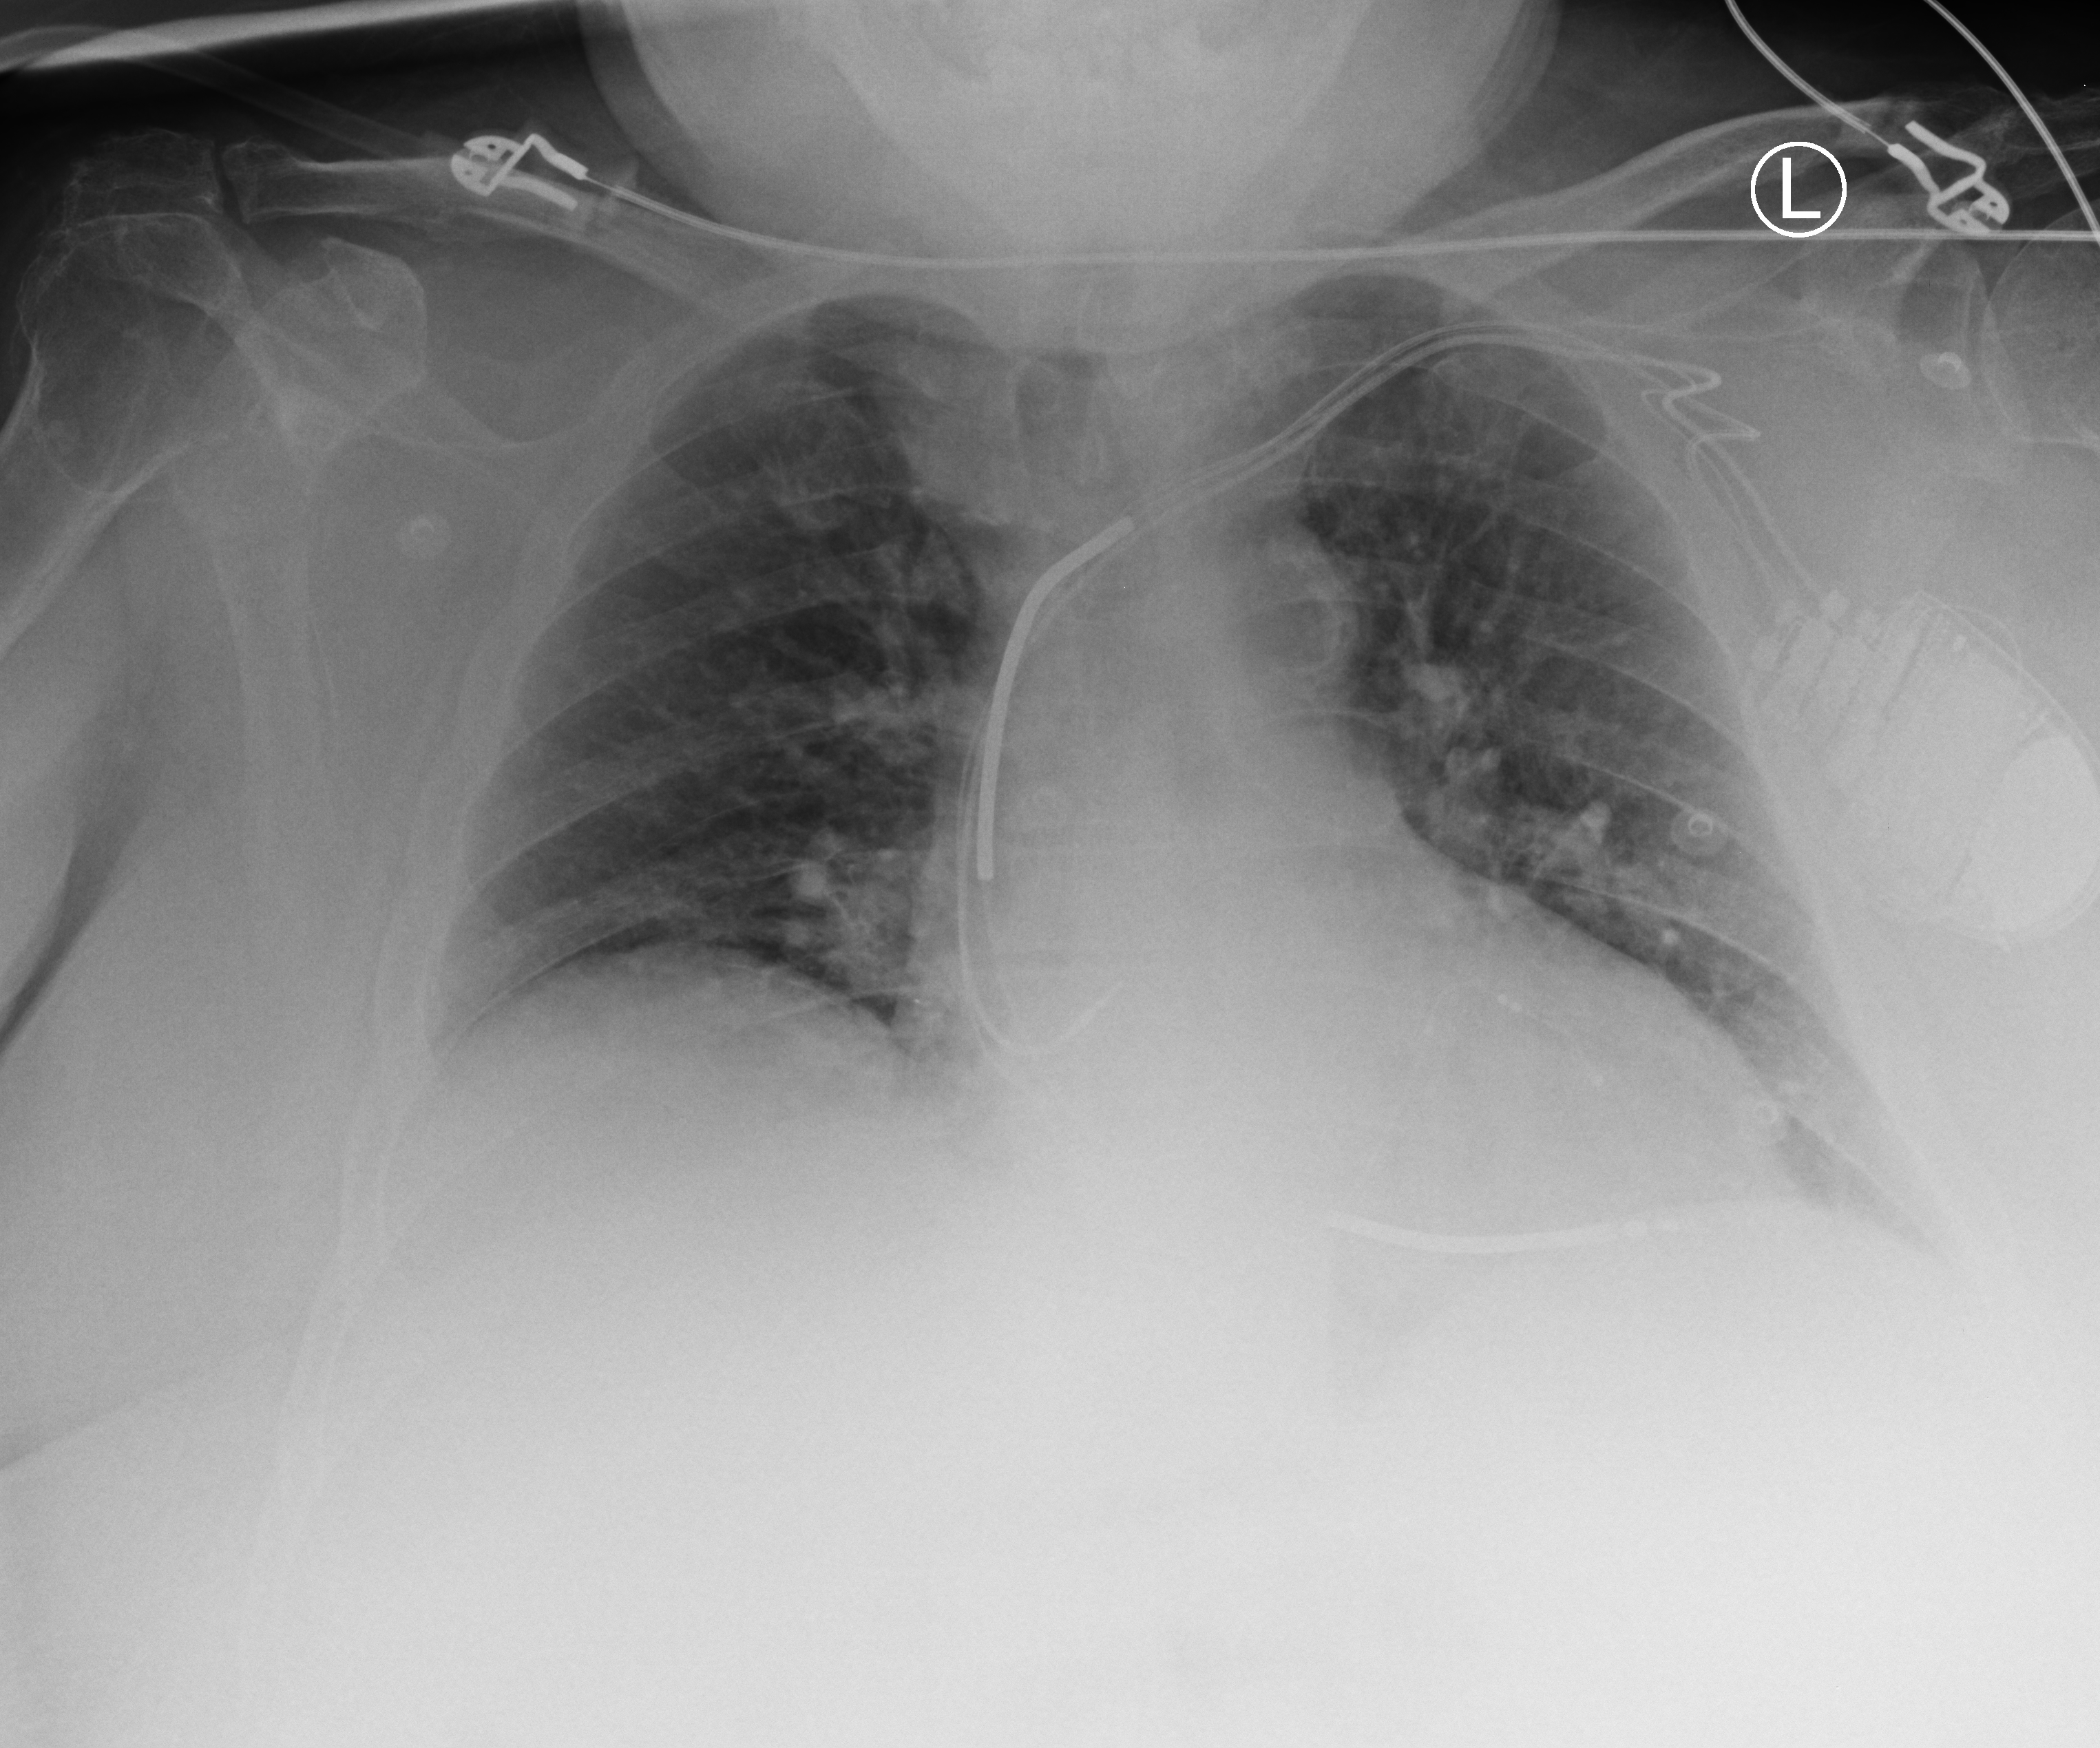
Bedside chest radiograph (computed radiography); anteroposterior (AP) projection. Patient hospitalised with COVID-19; male, aged 75–90 years.
From the hospital-stay record, not from the radiograph (when in the stay this image was taken is not recorded): mechanically ventilated during this hospital stay: no.